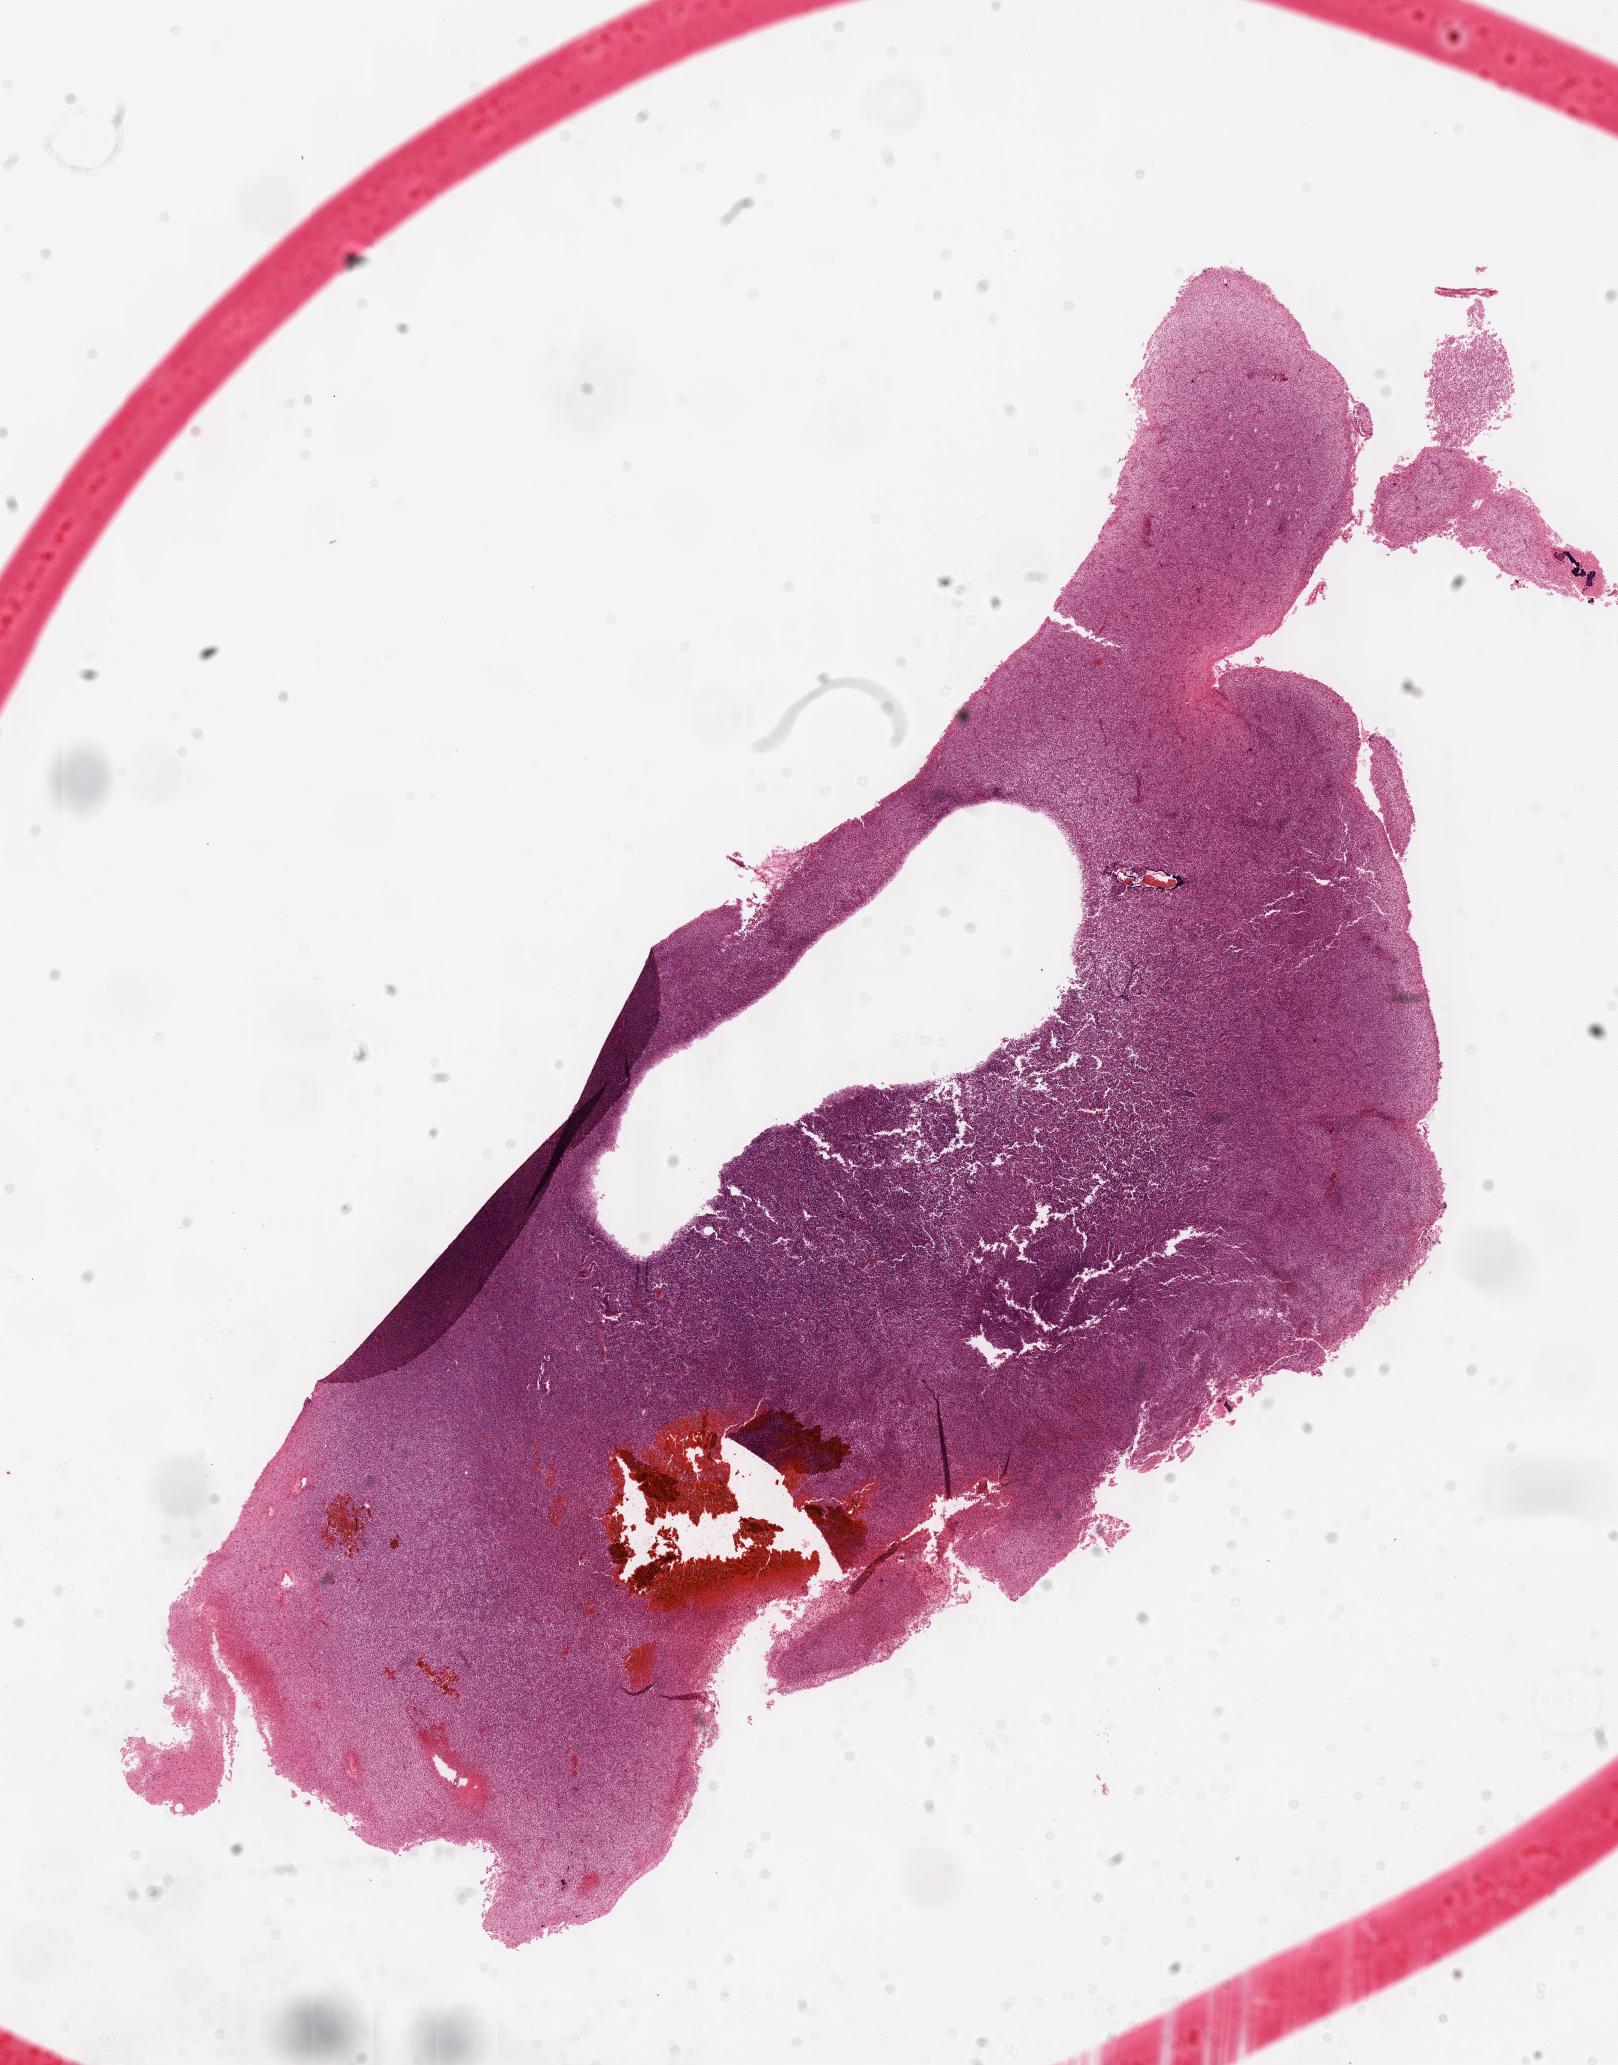
H&E-stained whole-slide image — whole scanned area (about 13.1 x 16.7 mm, from a 40x scan) shown as a low-resolution overview; formalin-fixed paraffin-embedded (FFPE) diagnostic section; sample: primary tumour, brain. Male patient; age at initial diagnosis 34 years. Histologic grade: G2 (moderately differentiated).
Pathologic diagnosis: Oligodendroglioma, NOS (cerebrum).